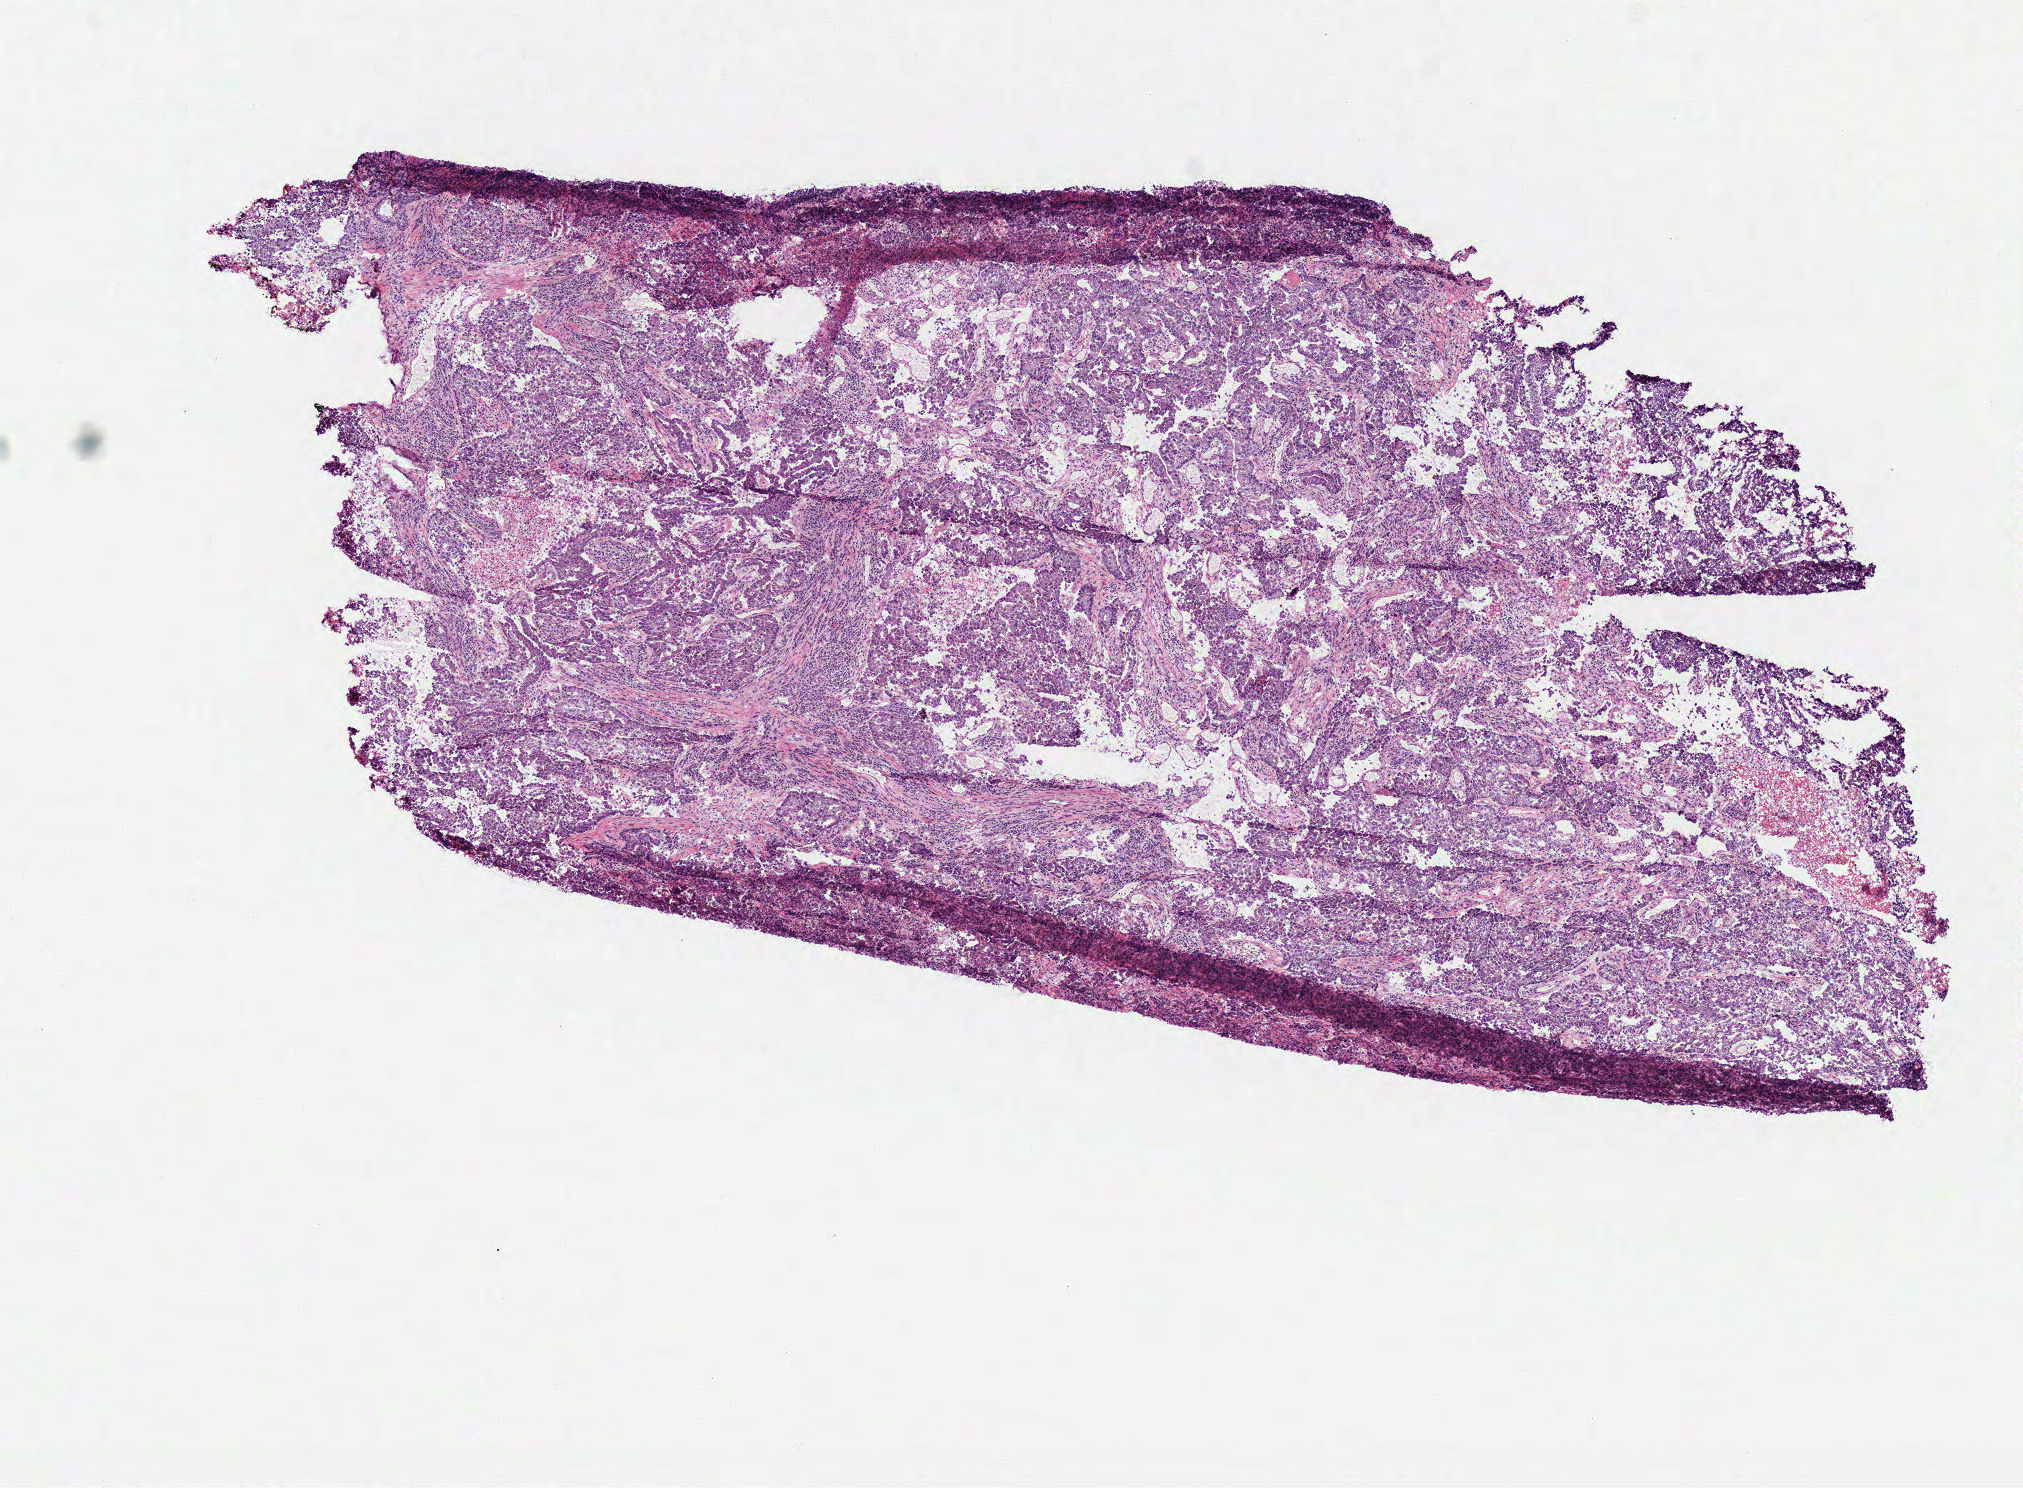
H&E whole-slide image, low-resolution overview of the scanned area, about 8.0 x 5.9 mm (slide scanned at 40x). Frozen section from the top of the tissue portion. Lung, primary tumour sample. Patient: female, age at initial diagnosis 60 years. Composition of this section per pathologist review: tumour cells 82%, tumour nuclei 70%, normal cells 0%, stromal cells 10%, necrosis 8%.
* AJCC pathologic stage: IA (6th edition)
* pathologic diagnosis: Adenocarcinoma with mixed subtypes (upper lobe, lung)